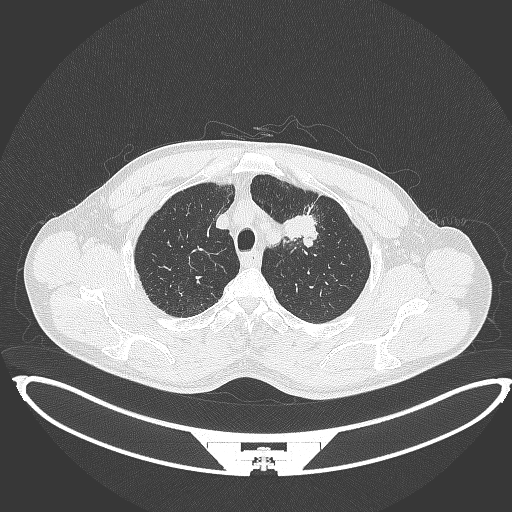
Chest CT, one axial slice; position 363 of 395 along the scan axis; 120 kVp; lung window (W 1500 / L -600 HU); 512 × 512 image matrix, field of view 457 × 457 mm. Male patient, age 60 years. Case-level facts recorded for this patient, not image findings: clinical TNM (as recorded): T2a N0 M0; histopathological grade: G1-G2.
Structures marked on this image (bounding box drawn by a radiologist):
- lung tumour (recorded histology: squamous cell carcinoma): bounding box (x1, y1, x2, y2) in pixels: (284, 210, 319, 241)